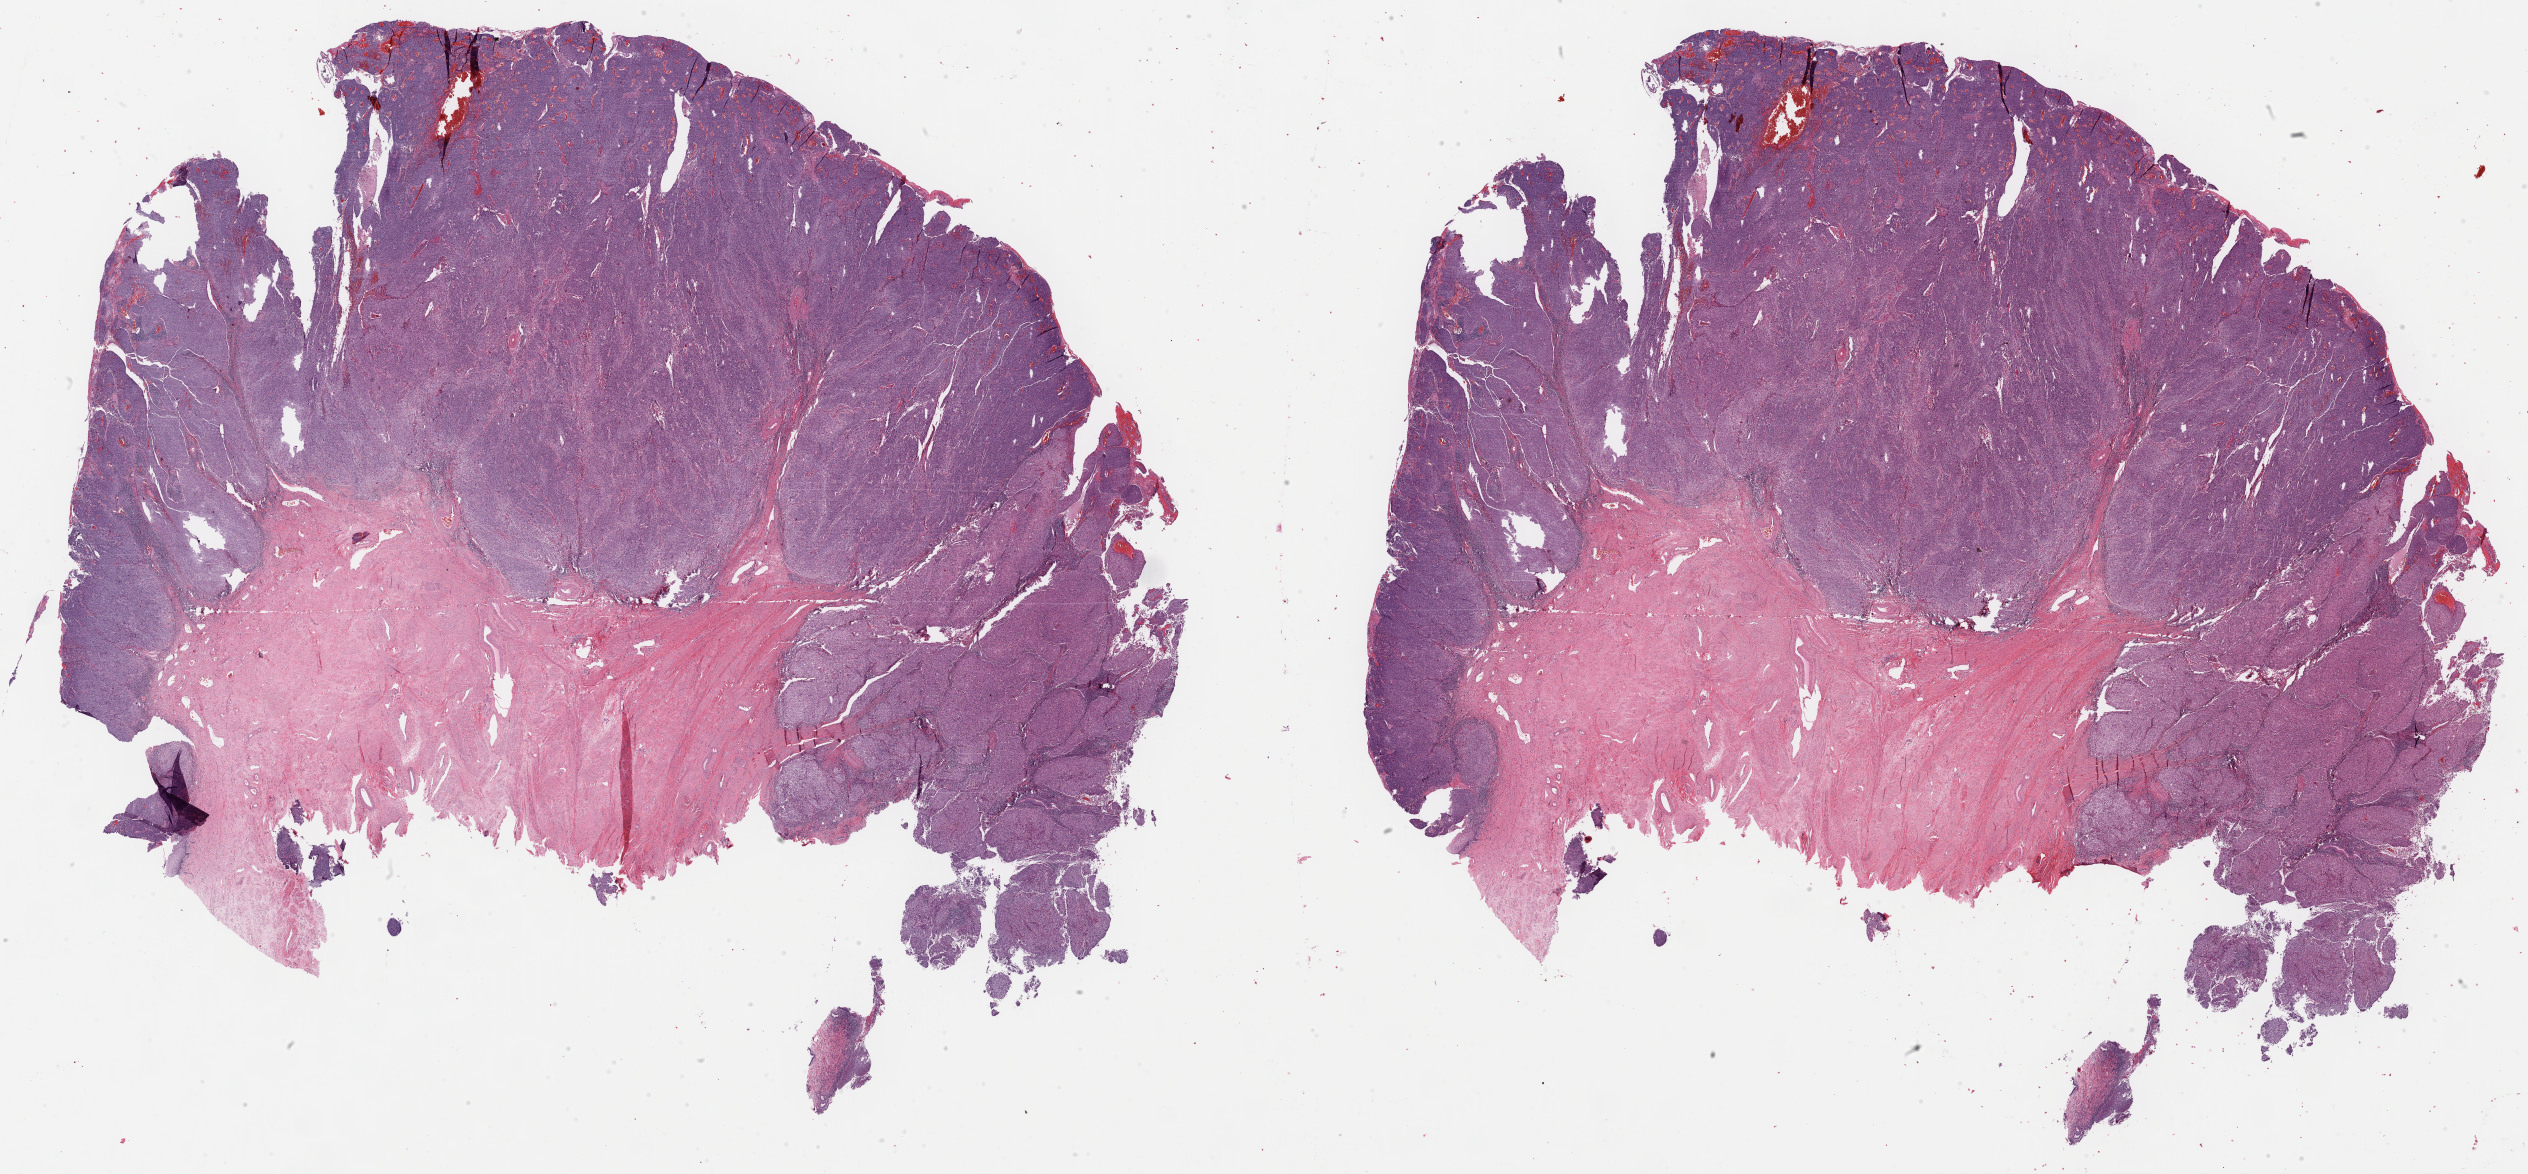
Digitized Hematoxylin and eosin (H&E) stained tissue section (whole slide) — shown as a low-resolution overview of the whole scanned area (about 39.9 x 18.5 mm, from a 40x scan), formalin-fixed paraffin-embedded (FFPE) diagnostic section, cervix, primary tumour sample. Patient: female, age at initial diagnosis 47 years. Histologic grade: G2 (moderately differentiated).
Lymph nodes positive (case pathology): 2 of 19 examined. FIGO stage: IB. Histologic diagnosis: Squamous cell carcinoma, NOS.